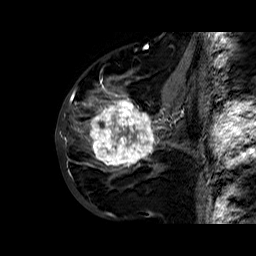
Breast MRI (dynamic contrast-enhanced), one sagittal slice. Slice 26 of 60 in the series (ordered by position). Dynamic contrast-enhanced series, time point 2 of 6 at this slice position (early post-contrast). 1.5 T. TE 6.4 ms, TR 32.8 ms. 4 mm slice thickness. 256 × 256 image matrix, field of view 200 × 200 mm. Female patient. From the clinical record (not read from this slice): setting: breast cancer imaged before/during neoadjuvant chemotherapy; receptor status: HR-positive, HER2-negative.
Structures marked on this image (semi-automatically segmented with operator editing):
- analysis volume of interest (the breast-tissue region the enhancement analysis was run in; not a lesion): bounding box <86,77,163,177> (left, top, right, bottom; pixels)
- tumour enhancement mask (voxels above the 100 % enhancement threshold inside the analysis volume of interest): <89,80,162,168>